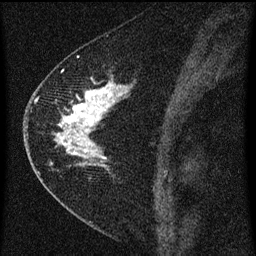
Breast MRI (dynamic contrast-enhanced), one sagittal slice. Slice 32 of 60 in the series (ordered by position). Dynamic contrast-enhanced series, image 2 of 3 at this slice position (ordered by acquisition). 1.5 T. TE 4.2 ms, TR 8 ms. 2 mm slice thickness. 256 × 256 image matrix. Female patient, age 47 years.
Structures marked on this image (semi-automatically segmented with operator editing):
- analysis volume of interest (the breast-tissue region the enhancement analysis was run in; not a lesion): bounding box (x1, y1, x2, y2) in pixels: (38, 76, 133, 193)
- tumour enhancement mask (voxels above the 70 % enhancement threshold inside the analysis volume of interest): (55, 84, 126, 167)